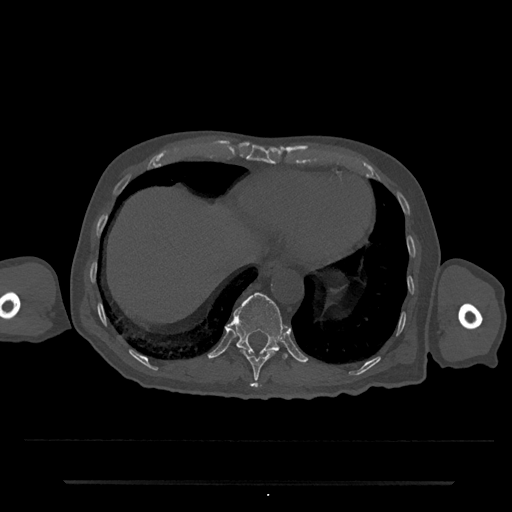
CT including the spine, one axial slice. Position 282 of 797 along the scan axis. Reconstruction kernel Br40s/3. 120 kVp. Bone window (W 1800 / L 400 HU). 0.5 mm slice thickness. 512 × 512 image matrix. Male patient, age 74 years. Case-level facts recorded for this patient, not image findings: primary cancer: prostate.
Annotated regions visible in this slice (semi-automatic segmentation, software-assisted and operator-edited):
- T10 vertebra: bounding box <240,350,277,388> (left, top, right, bottom; pixels)
- T11 vertebra: <228,292,287,359>